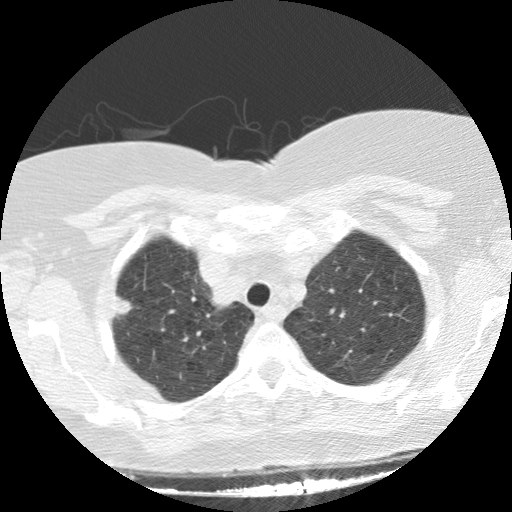
Chest CT (low-dose screening protocol), one axial image. Baseline screening round. Lung window (W 1500 / L -600 HU). Slice 23 of 136 in the series. Female, age 64 years at enrolment.
• Lesion marked by an expert reader, bounding box (x1, y1, x2, y2) in pixels: (99, 280, 146, 330).
• Reader record for this screening exam (exam-level; its link to the box is not recorded): non-calcified nodule or mass ≥4 mm, right upper lobe, 17 × 16 mm, spiculated (stellate) margins, soft tissue attenuation.
• Participant outcome: lung cancer diagnosed 70 days after this screen — adenocarcinoma, NOS, right upper lobe, stage IIIA (AJCC 6th edition), 15 mm at pathology.